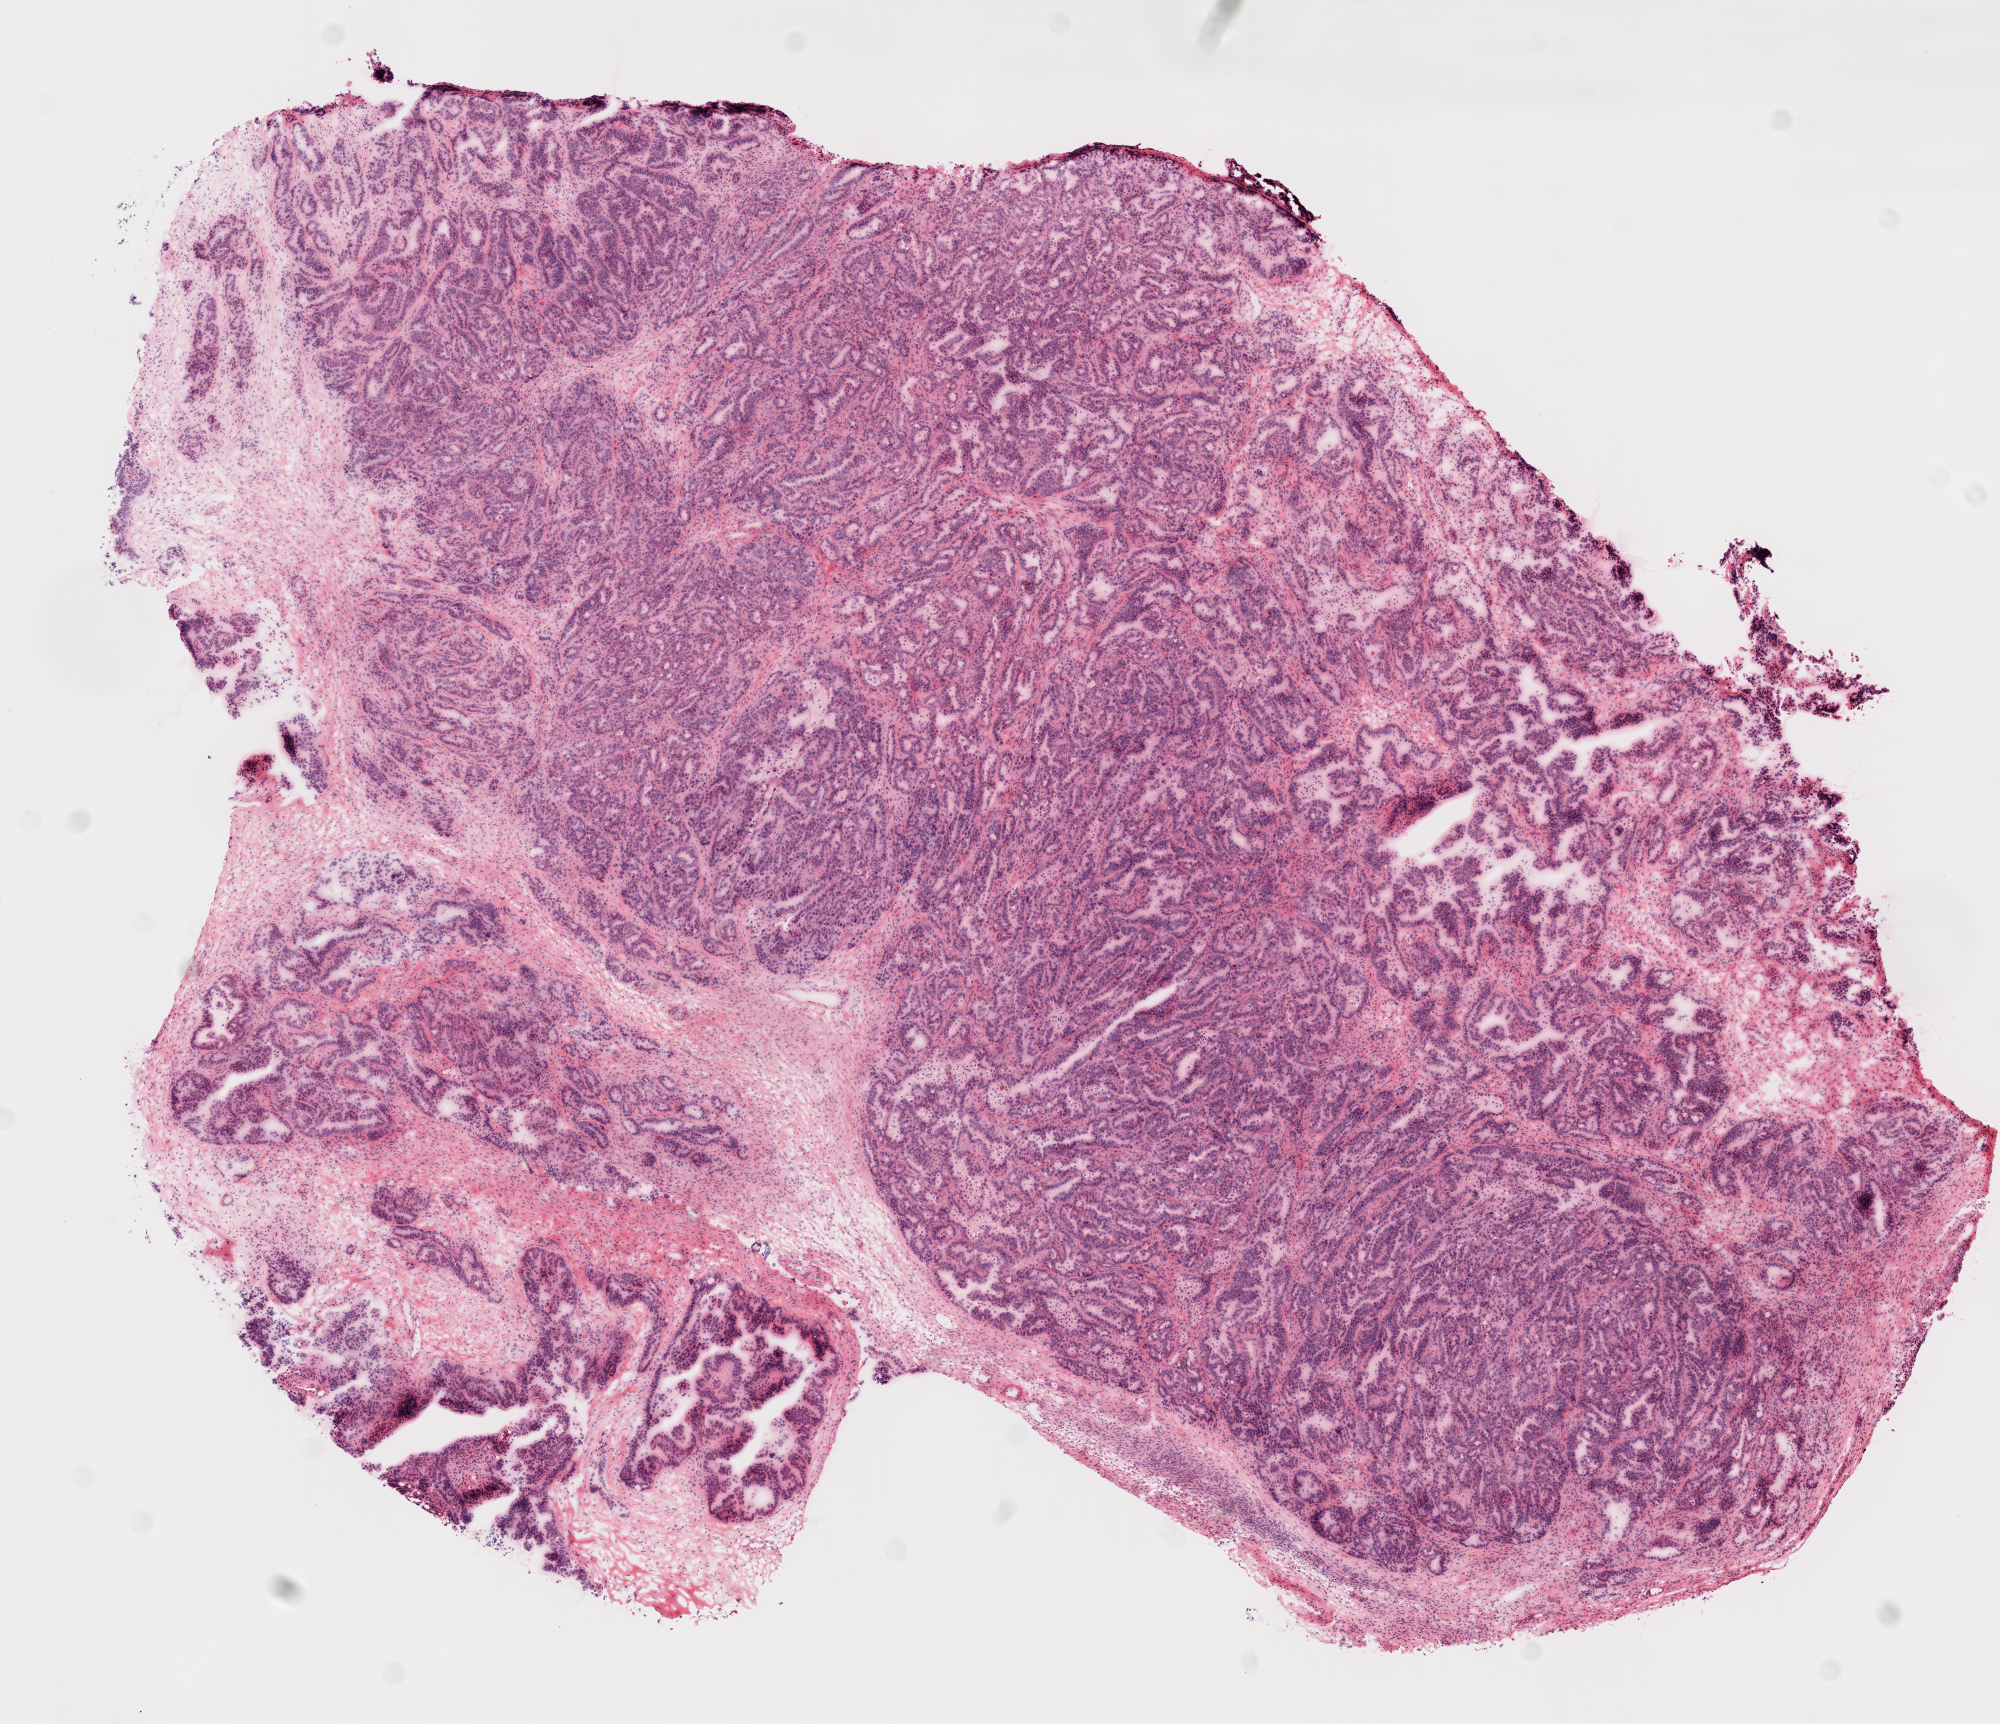
Digitized H&E-stained tissue section (whole slide), shown as a low-resolution overview of the whole scanned area (about 8.0 x 6.9 mm, slide scanned at 20x). Frozen section from the top of the tissue portion. Primary tumour sample from the ovary. Patient: female, age at initial diagnosis 42 years. Histologic grade: G3 (poorly differentiated). Slide review estimates, as recorded: tumour cells 90%, tumour nuclei 98%, normal cells 0%, stromal cells 10%, necrosis 0%.
* FIGO stage: IIIC
* laterality: bilateral
* pathologic diagnosis: Serous cystadenocarcinoma, NOS